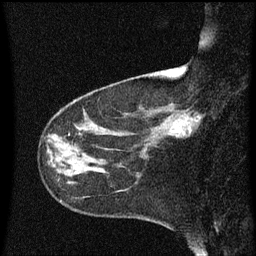
Breast MRI (dynamic contrast-enhanced), one sagittal slice. Position 19 of 60 along the scan axis. Dynamic contrast-enhanced series, image 2 of 3 at this slice position (ordered by acquisition). 1.5 T. TE 4.2 ms, TR 8.4 ms. 256 × 256 image matrix. Female patient, age 41 years. Case-level facts recorded for this patient, not image findings: setting: breast cancer imaged before/during neoadjuvant chemotherapy; receptor status: triple-negative.
Annotated regions visible in this slice (semi-automatically segmented with operator editing):
- analysis volume of interest (the breast-tissue region the enhancement analysis was run in; not a lesion): bounding box [x1, y1, x2, y2] px = [158, 100, 202, 145]
- tumour enhancement mask (voxels above the 70 % enhancement threshold inside the analysis volume of interest): [184, 118, 199, 135]